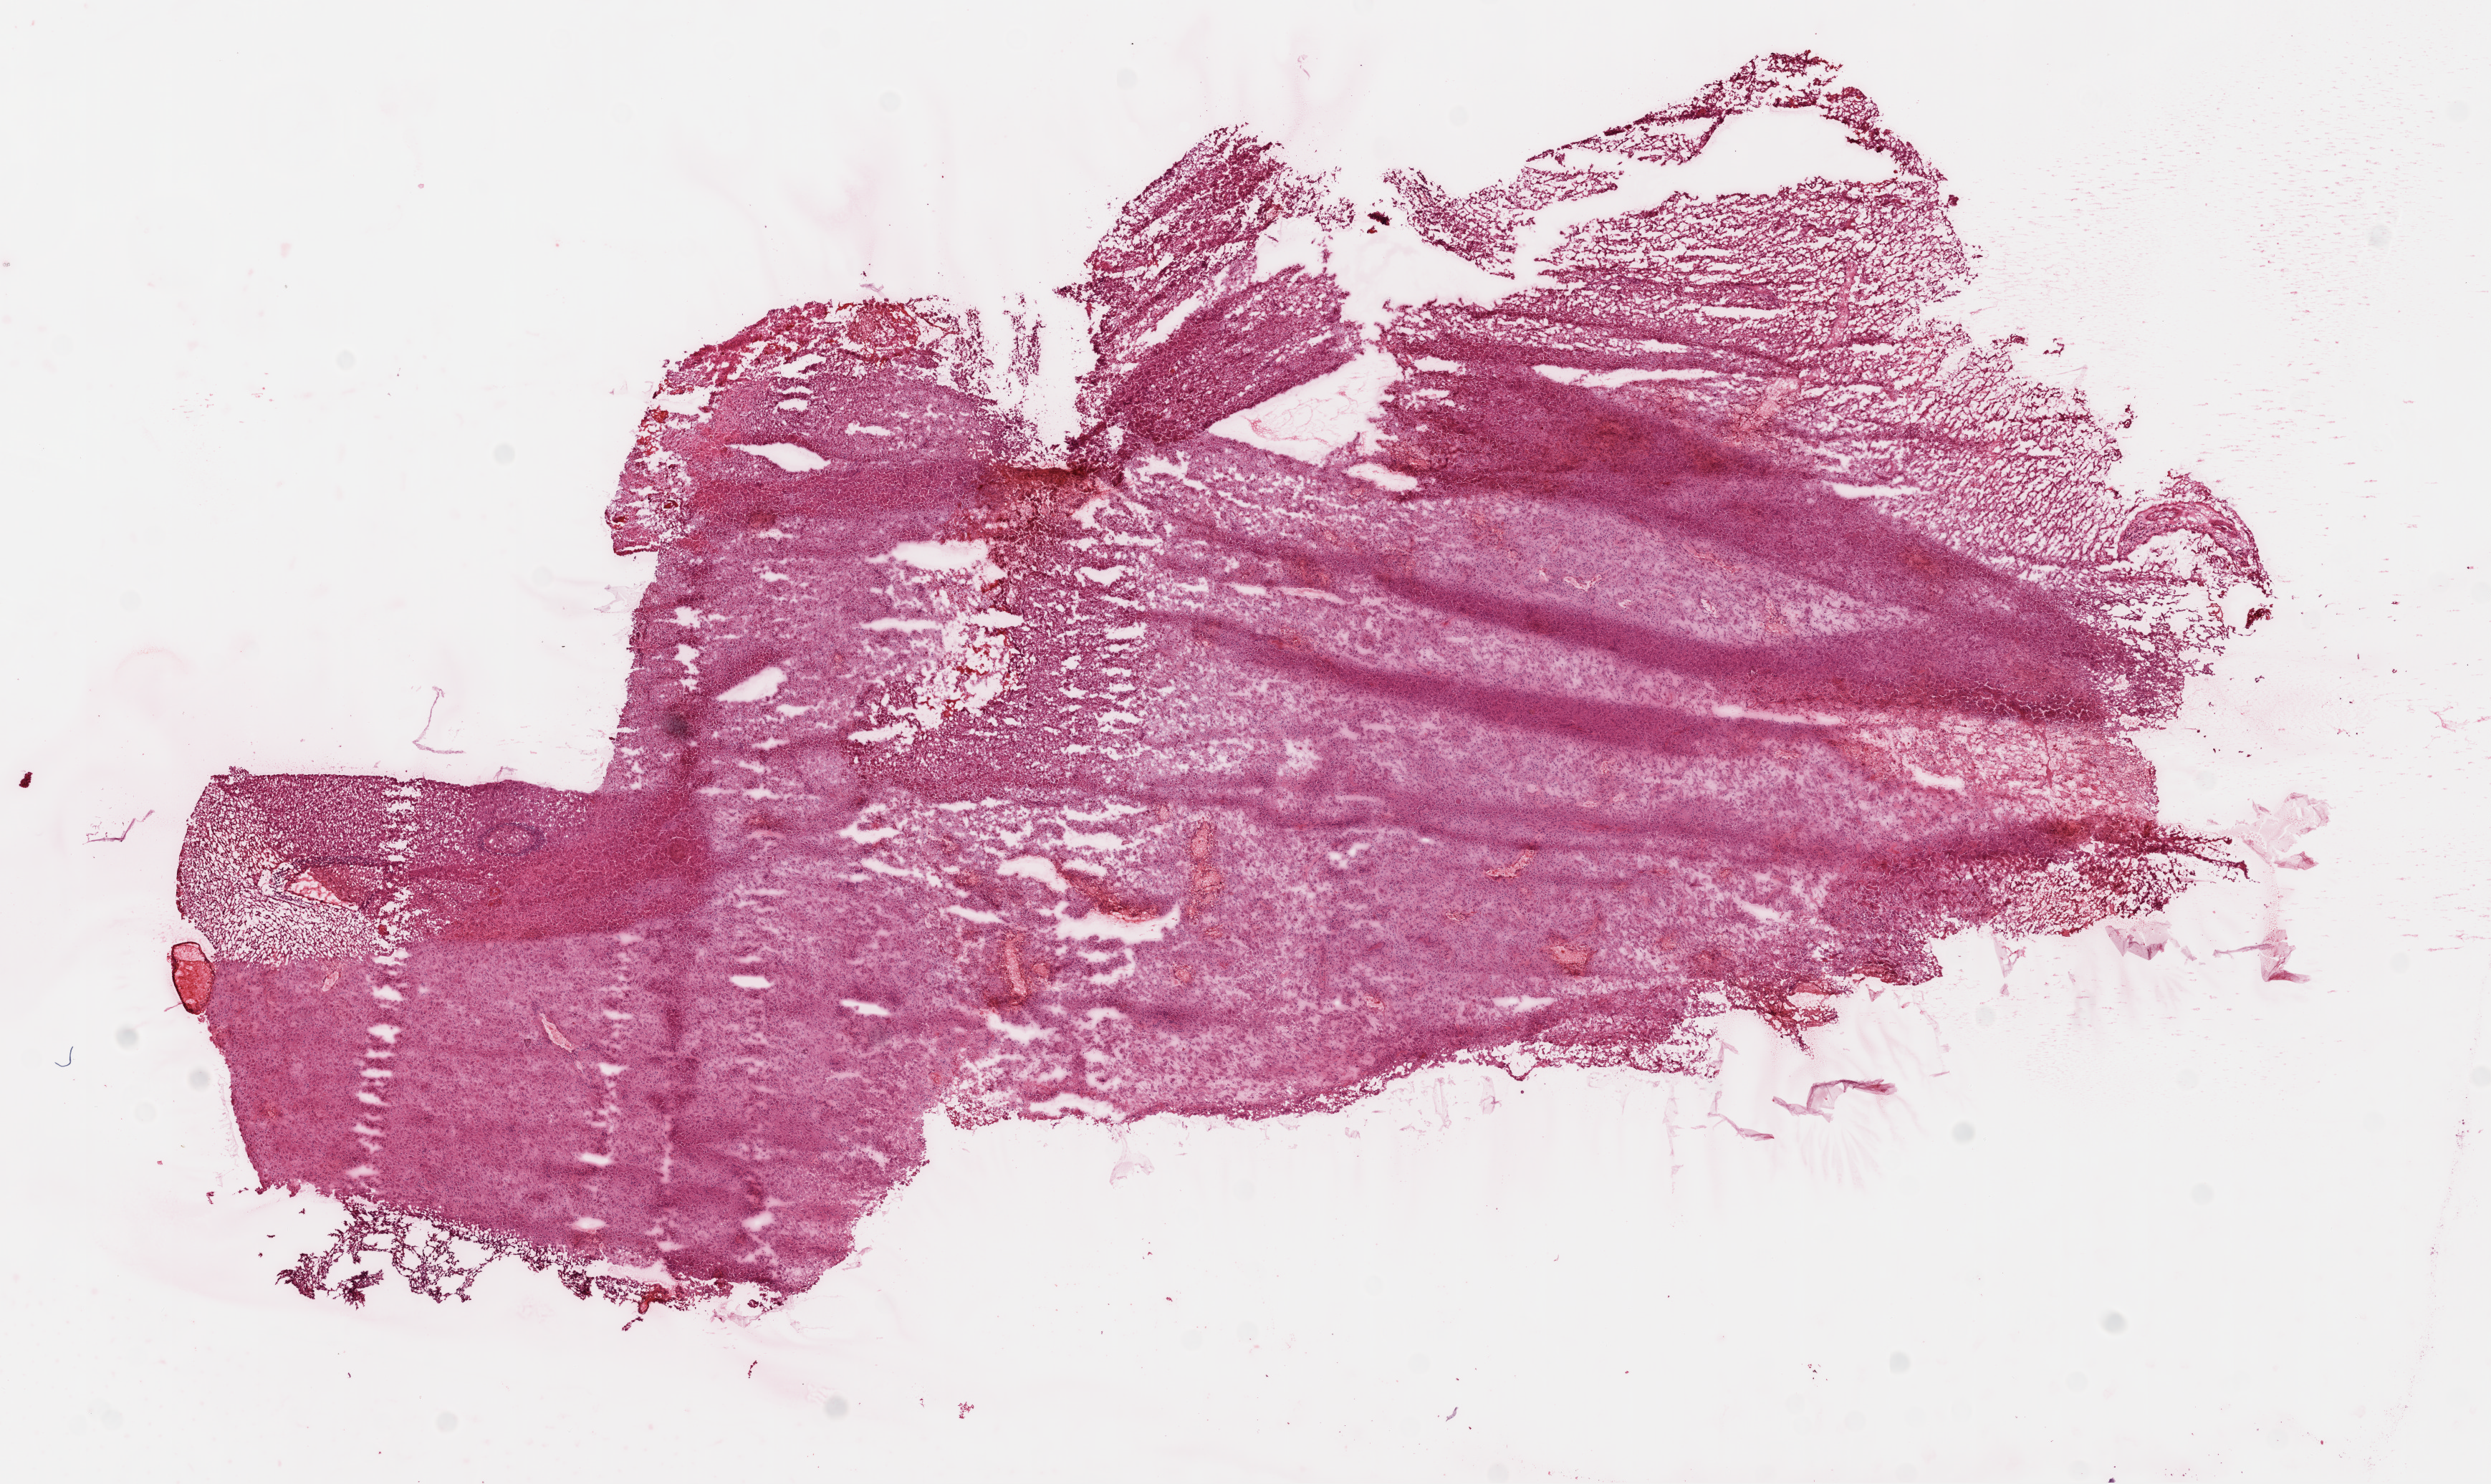
H&E whole-slide image — low-resolution overview of the scanned area, about 14.0 x 8.4 mm (acquisition: 20x scan), frozen section from the top of the tissue portion, sample: primary tumour, brain. Female patient; age at initial diagnosis 66 years. Slide review estimates, as recorded: tumour cells 80%, tumour nuclei 90%, stromal cells 15%, necrosis 5%.
Pathologic diagnosis: Glioblastoma.